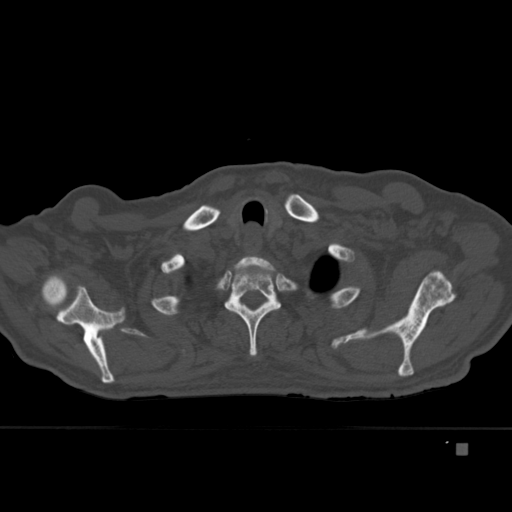
CT including the spine, one axial slice; slice 347 of 451 in the series (ordered by position); bone window (W 1800 / L 400 HU); 1.5 mm slice thickness; 512 × 512 image matrix, field of view 378 × 378 mm. Male patient, age 75 years. Case-level facts recorded for this patient, not image findings: primary cancer: prostate.
Structures marked on this image (semi-automatic segmentation, software-assisted and operator-edited):
- T1 vertebra: box from (x=236, y=256) to (x=276, y=271) px
- T2 vertebra: (x=224, y=257)–(x=281, y=356)